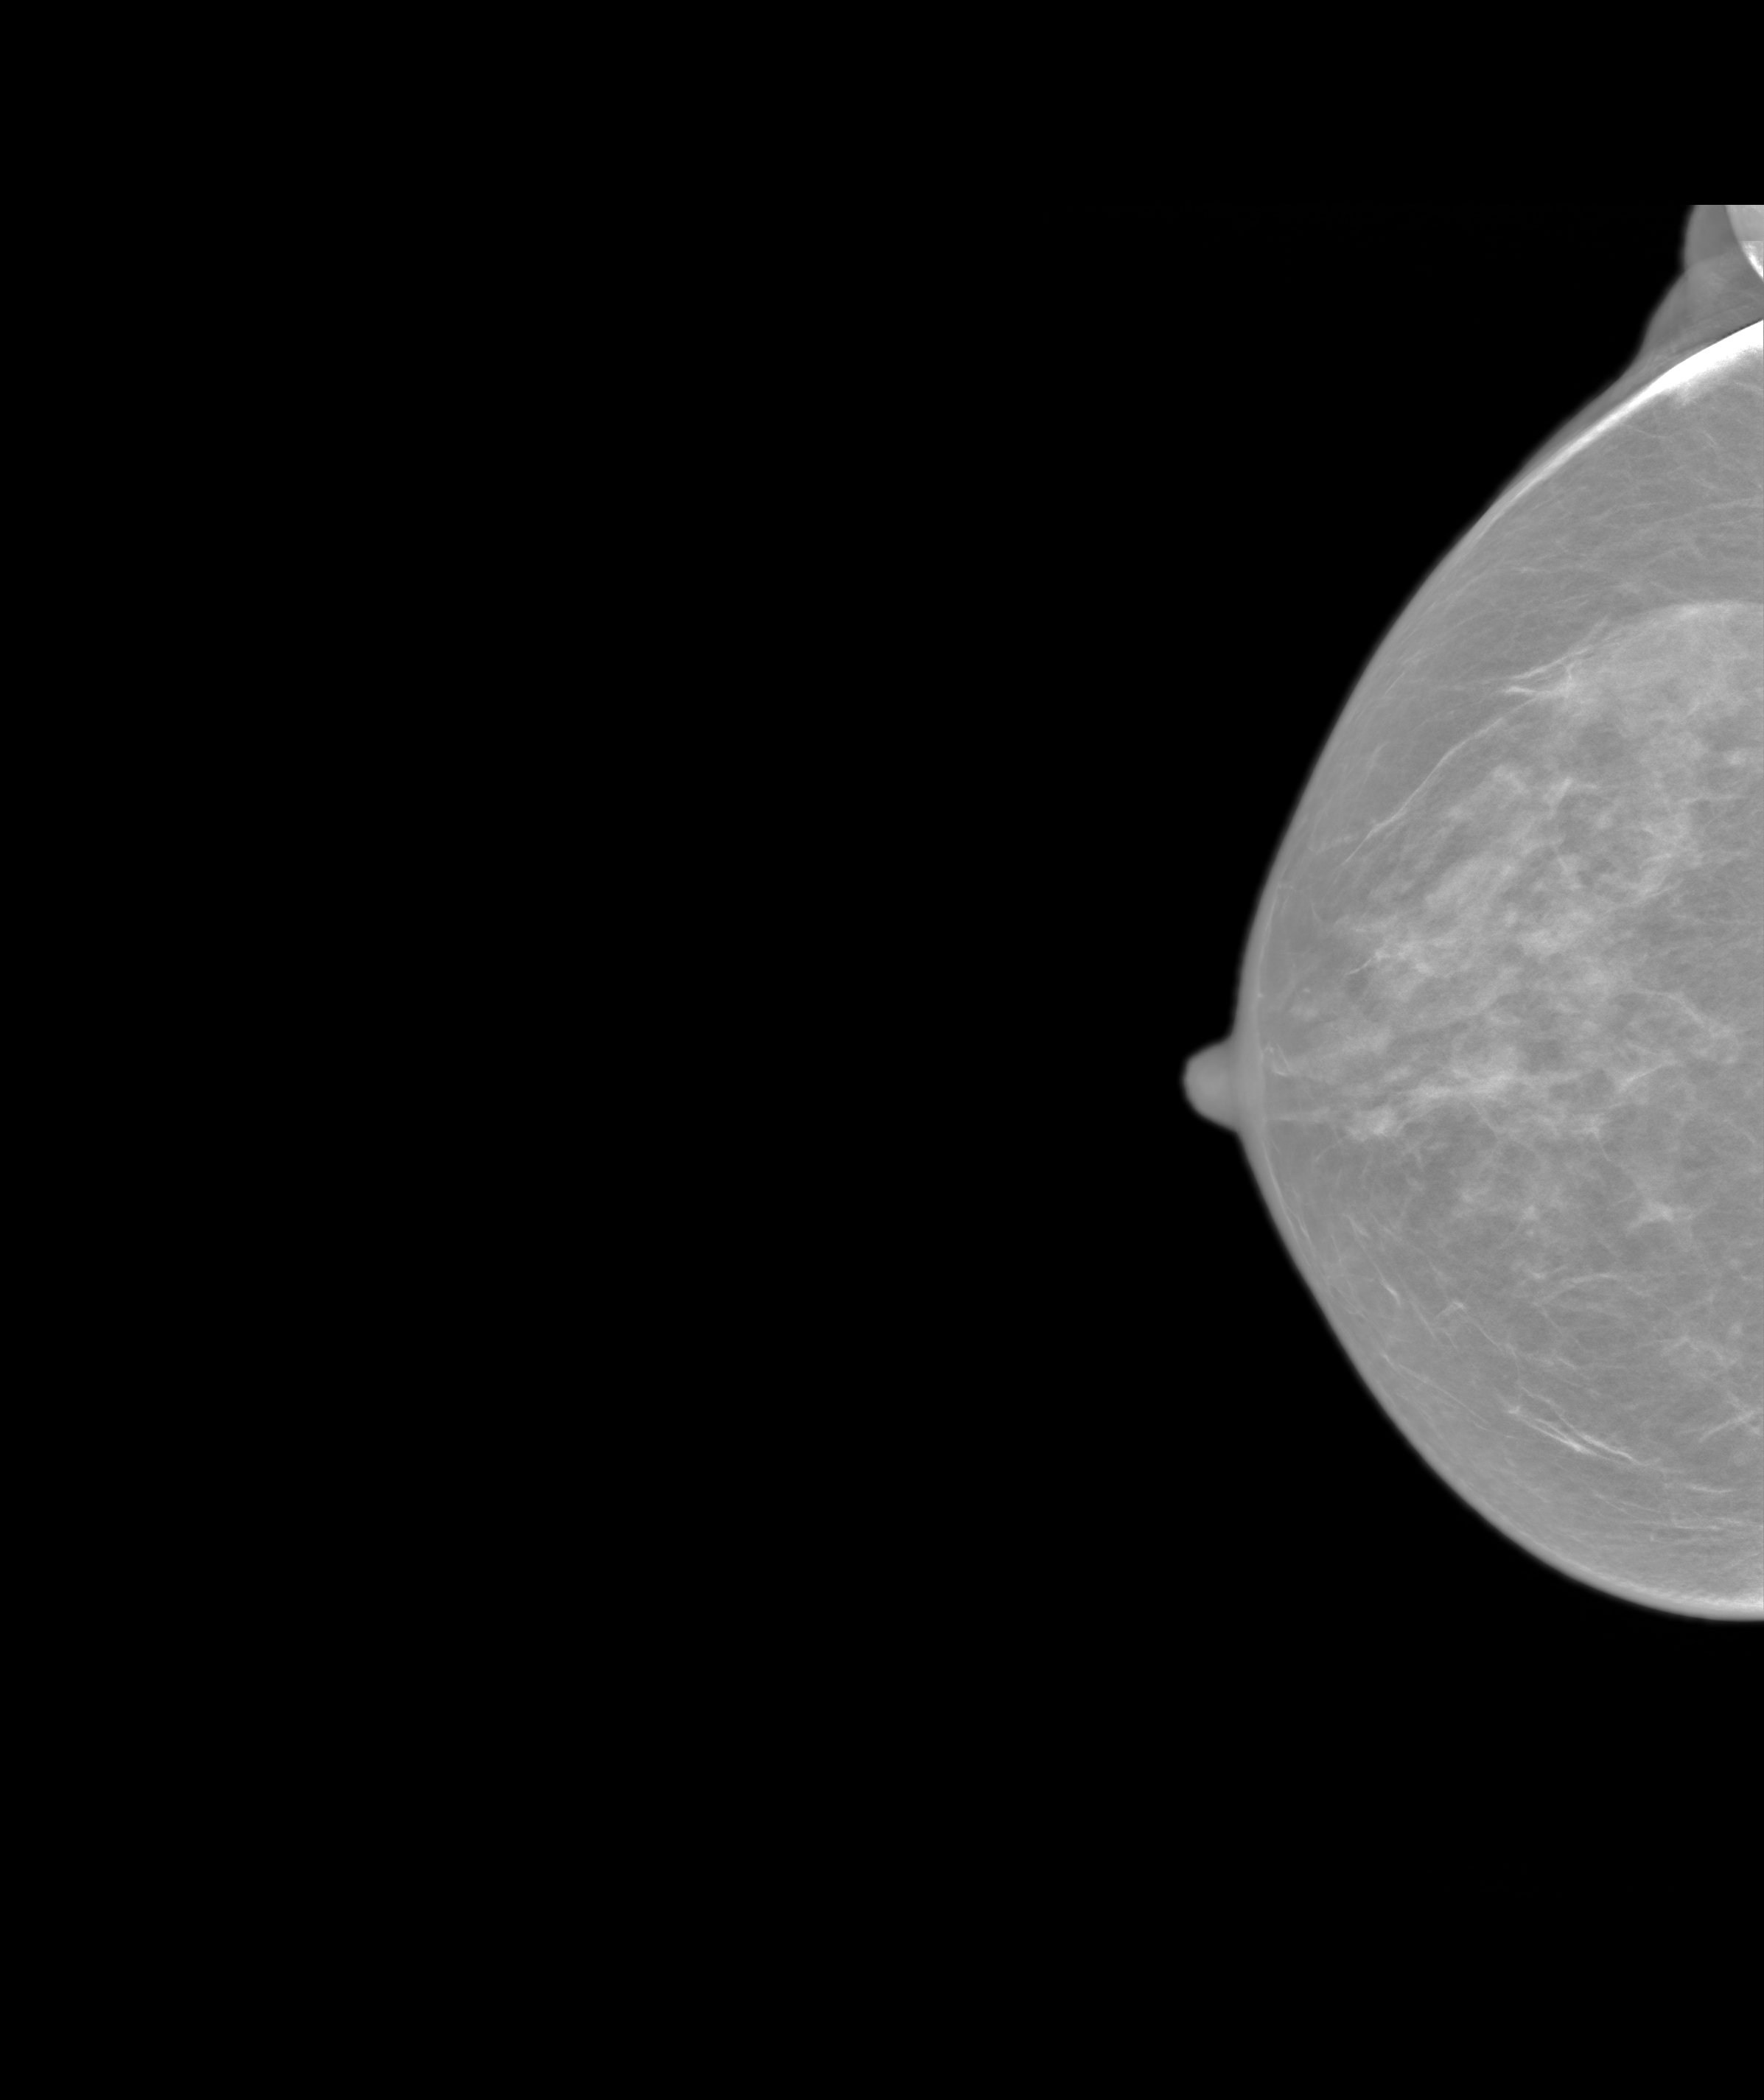
Annual screening mammography examination. Patient: female, 62 years.
Image type: synthesized 2-D view from tomosynthesis. Breast: right. Projection: cranio-caudal projection.